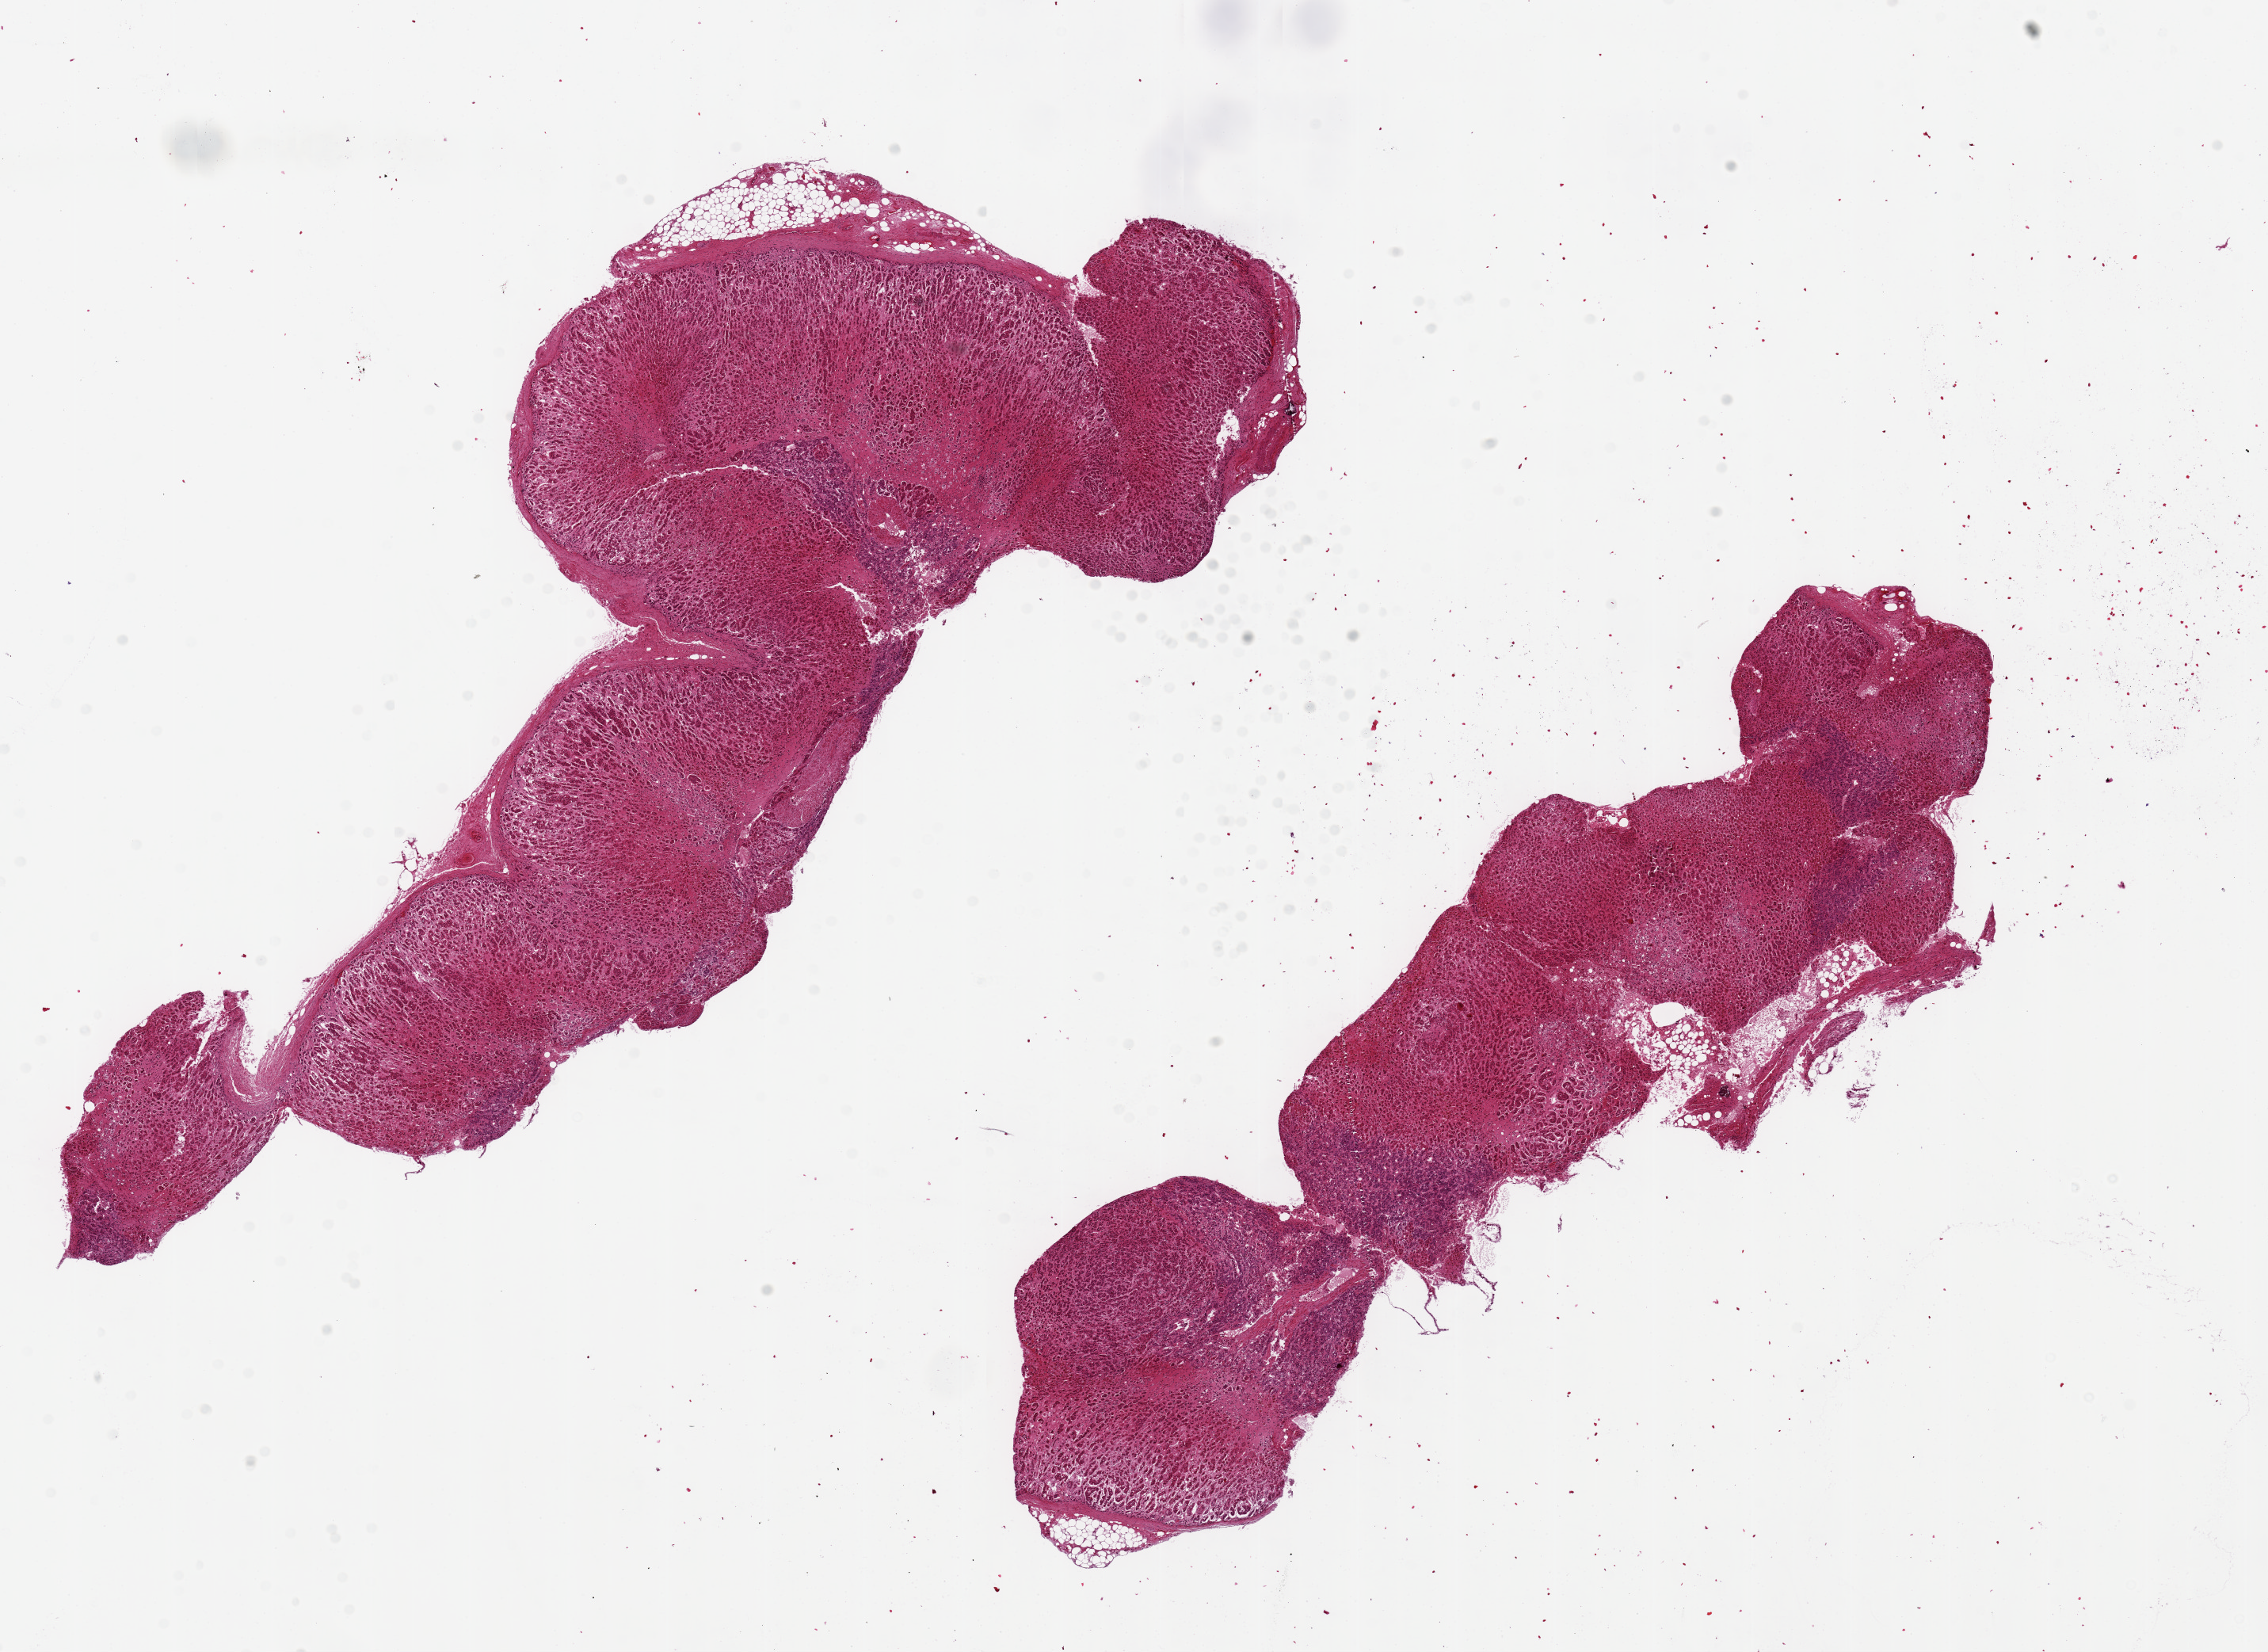
Hematoxylin and eosin (H&E) whole-slide image — low-resolution overview of the scanned area, about 22.6 x 16.5 mm (slide scanned at 20x). PAXgene-fixed, paraffin-embedded tissue. Target tissue: adrenal gland. Tissue donor sample. Donor sex: male.
* pathologist's review note for this sample: 2 pieces, 15x6 & 13x5mm; <10% adipose